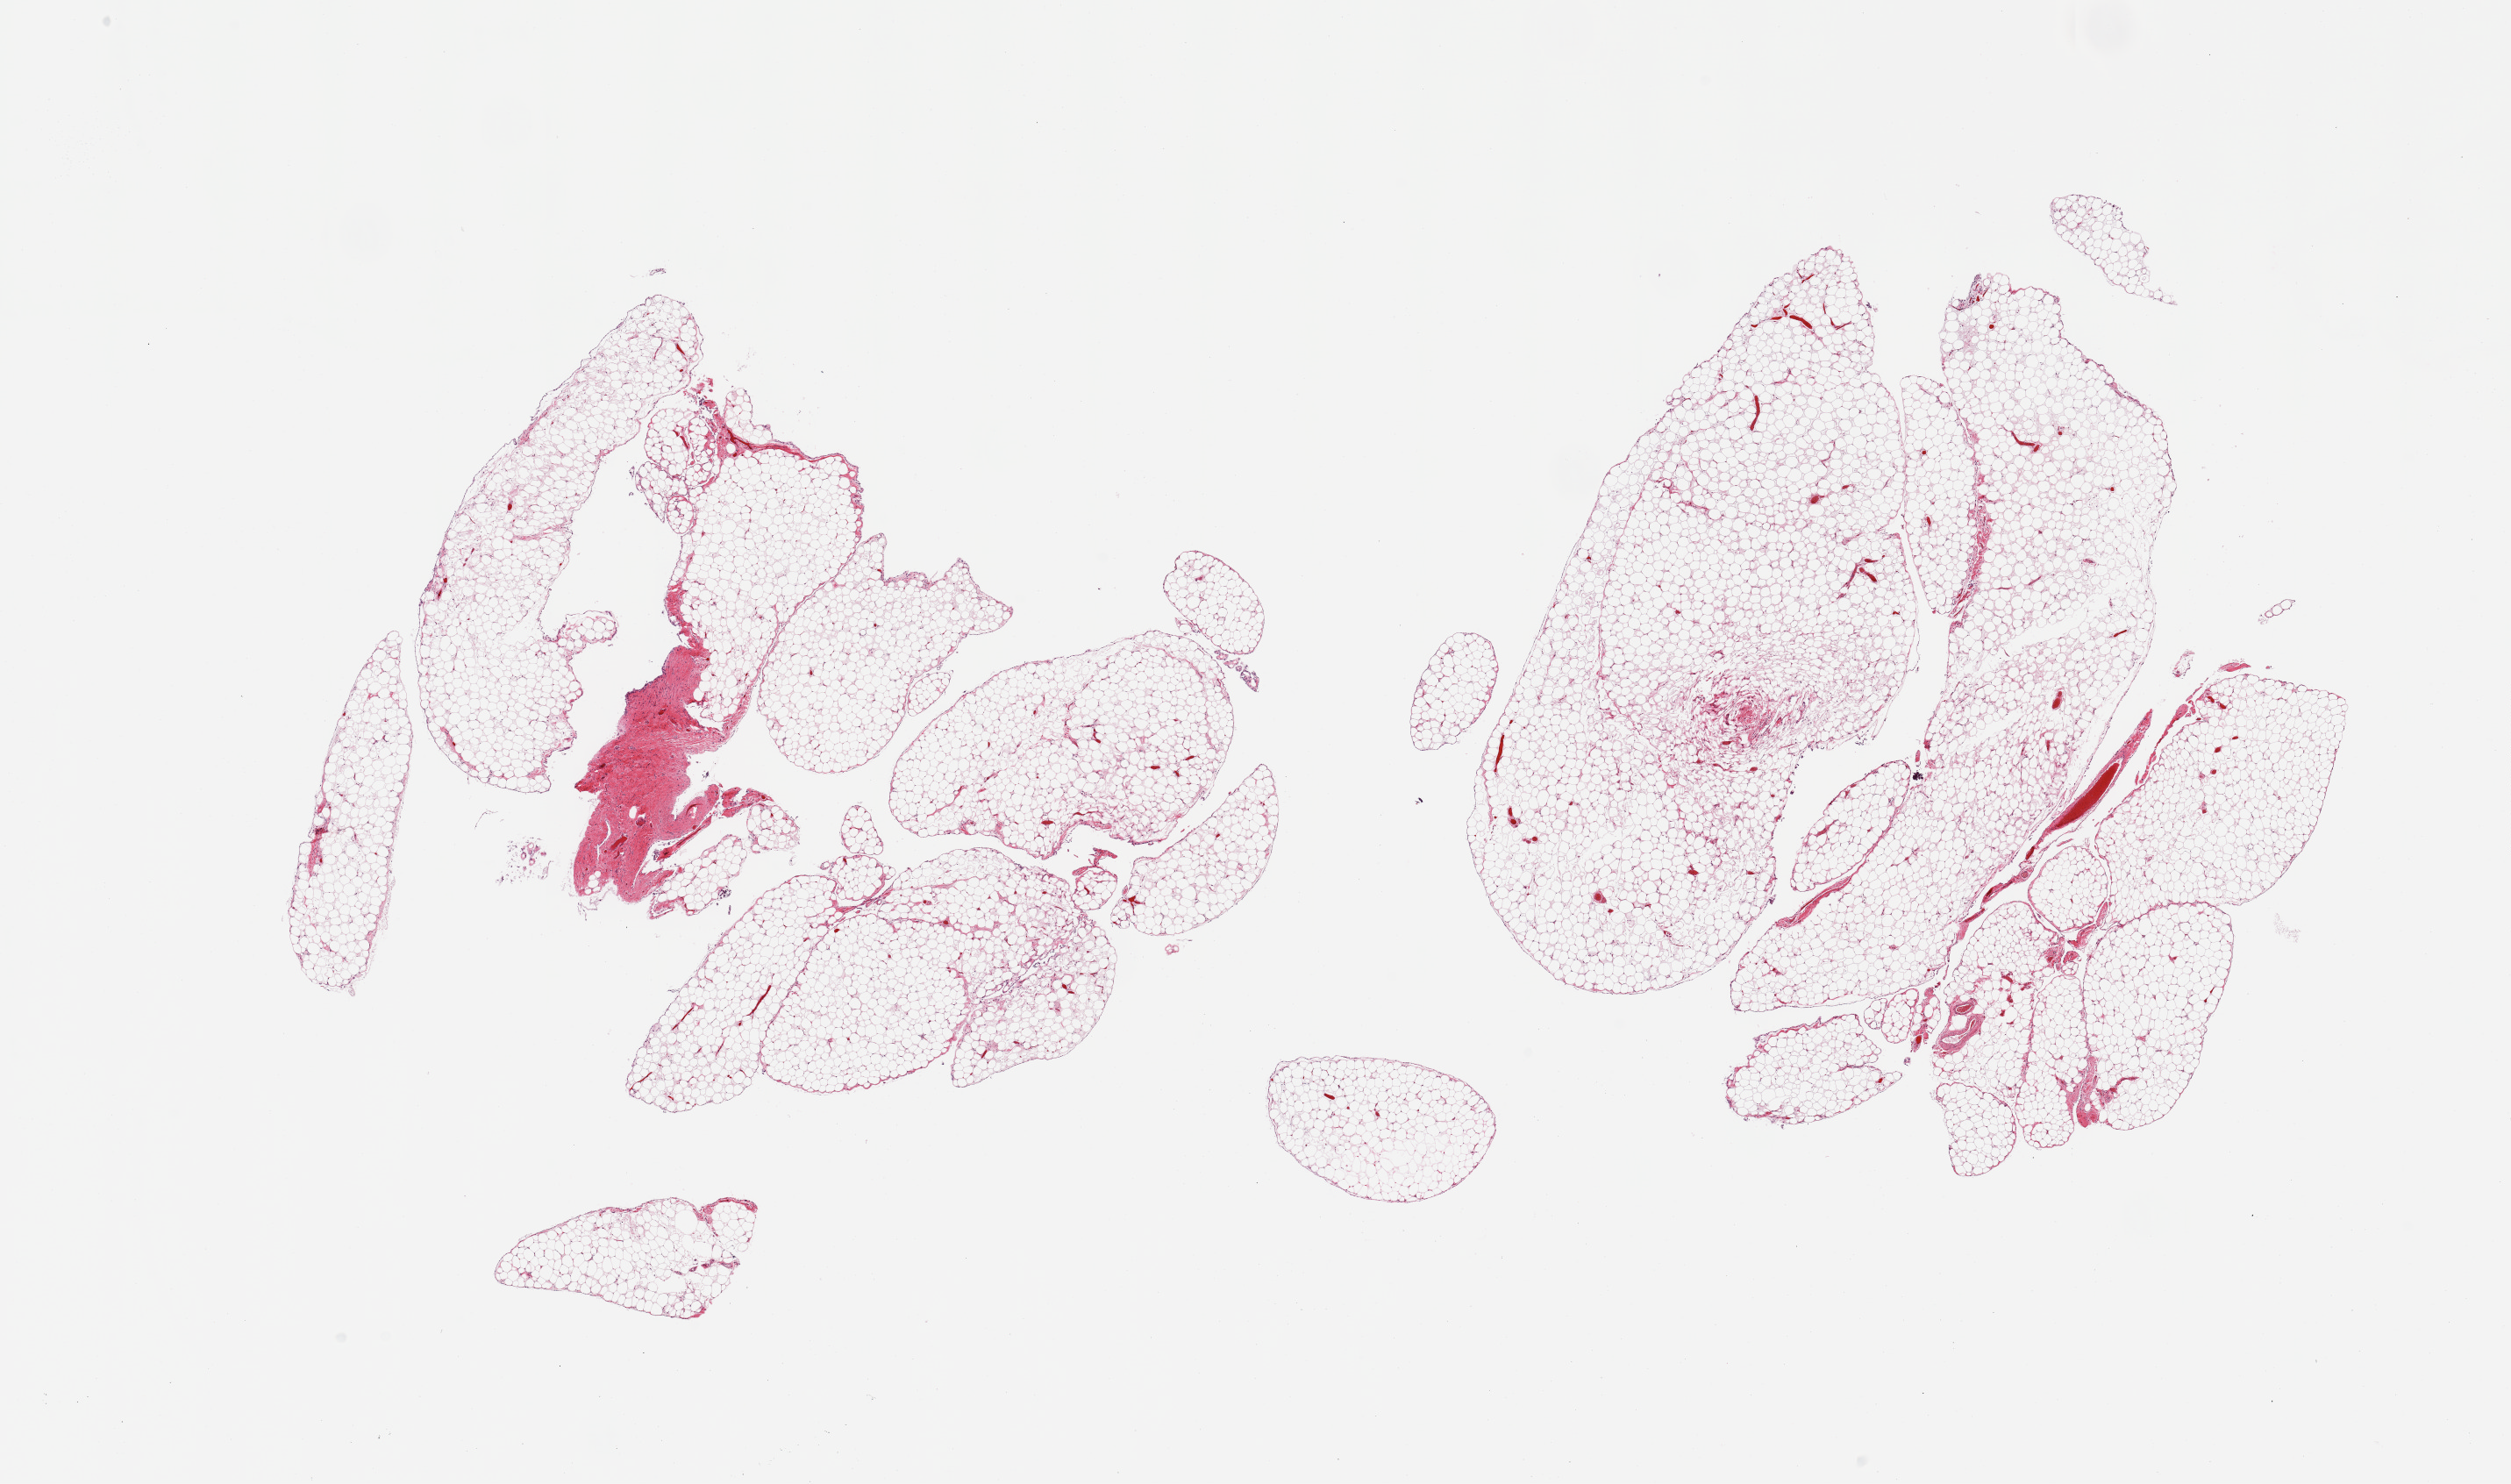
Whole-slide image, H&E stain, brightfield, a low-resolution overview of the entire scanned area, about 22.6 x 13.4 mm (from a 20x scan); PAXgene-fixed, paraffin-embedded tissue; section of omentum (target tissue); donor tissue sample. Donor sex: male.
Pathologist's review note for this sample: 2 pieces.